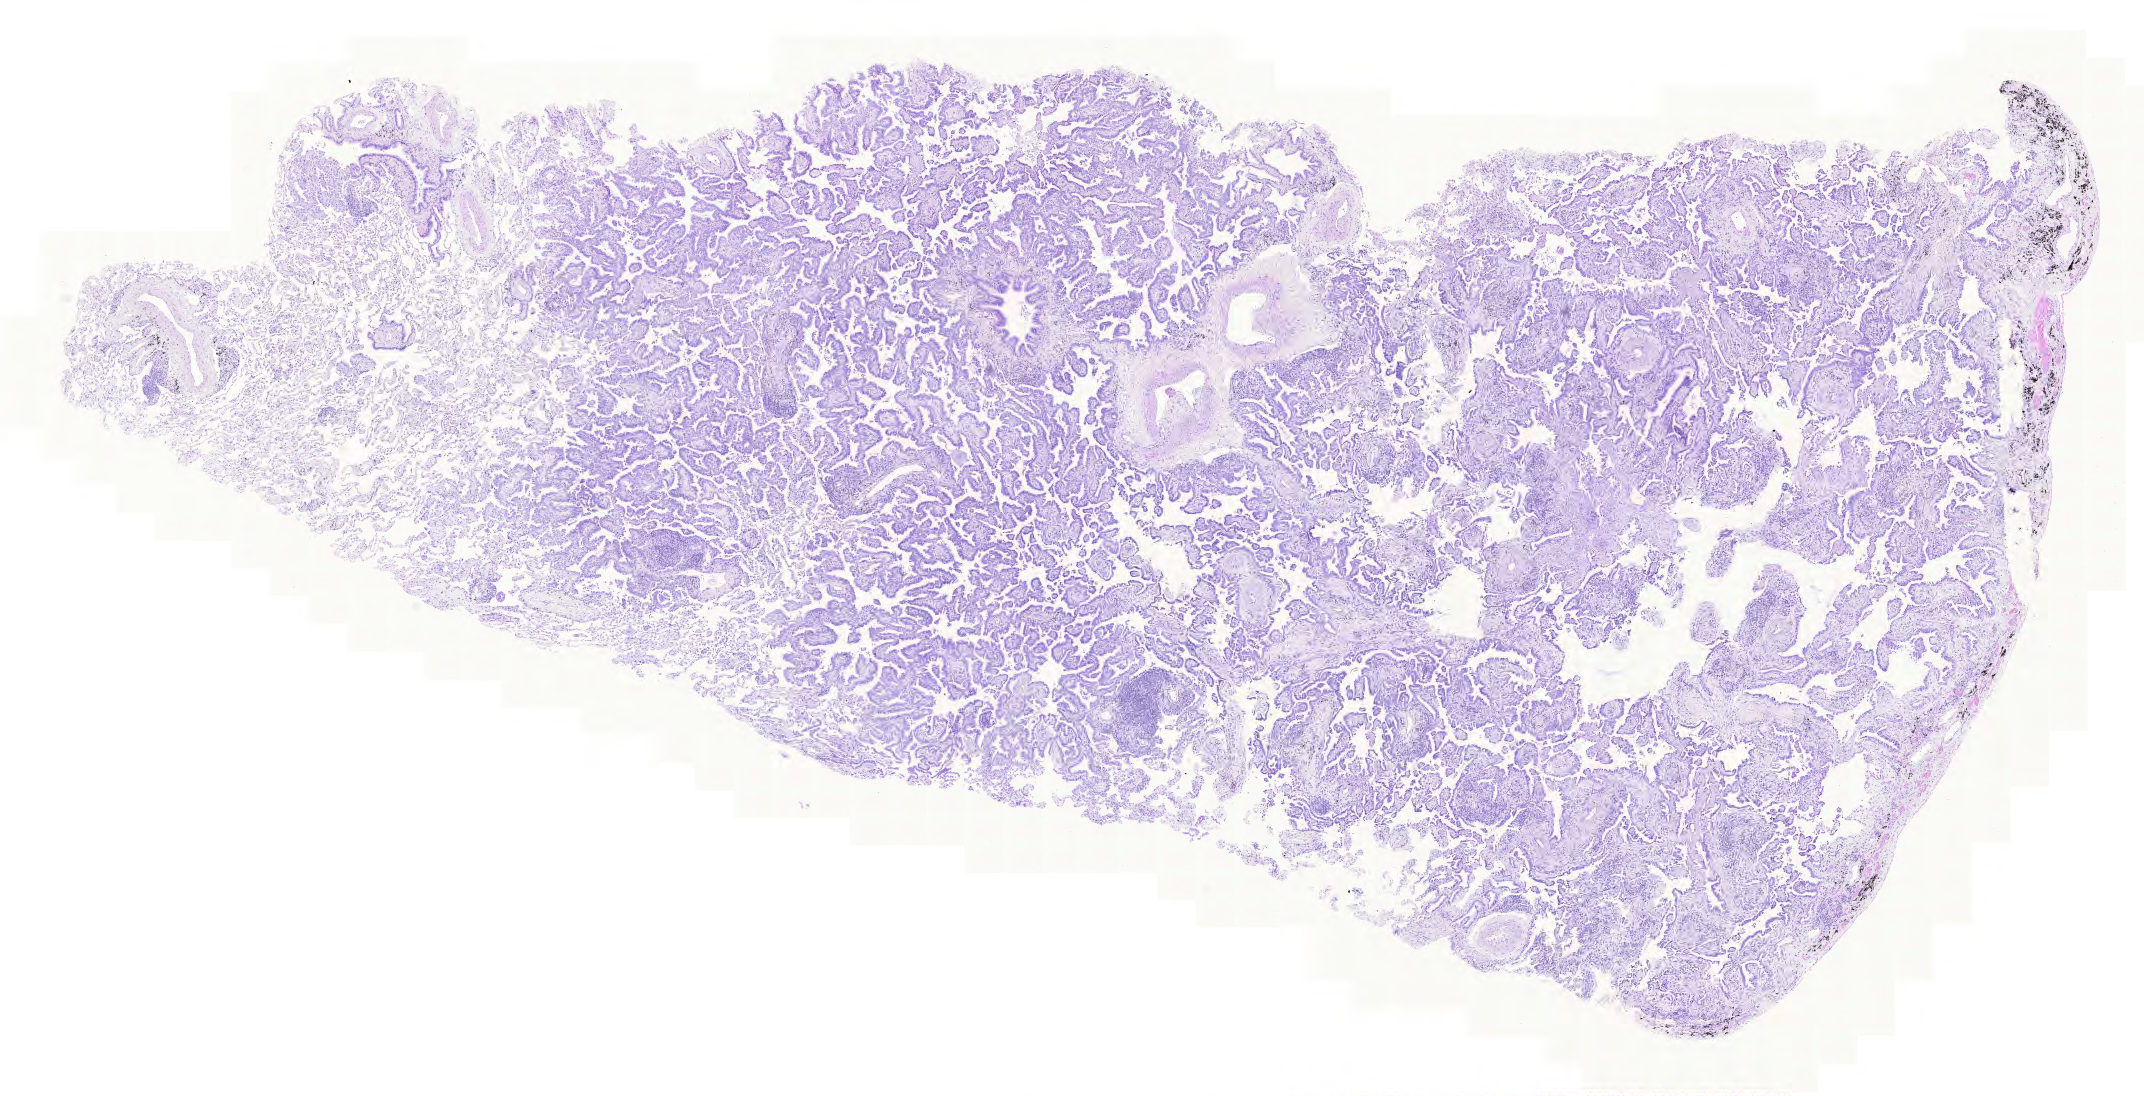
Whole-slide histology image, H&E — whole scanned area (about 16.0 x 8.2 mm) shown as a low-resolution overview; formalin-fixed paraffin-embedded (FFPE) diagnostic section; primary tumour sample from the lung. Male, age 67 years at initial diagnosis.
Histologic diagnosis: Adenocarcinoma, NOS (lower lobe, lung). AJCC pathologic stage: IB (6th edition). Laterality: right.